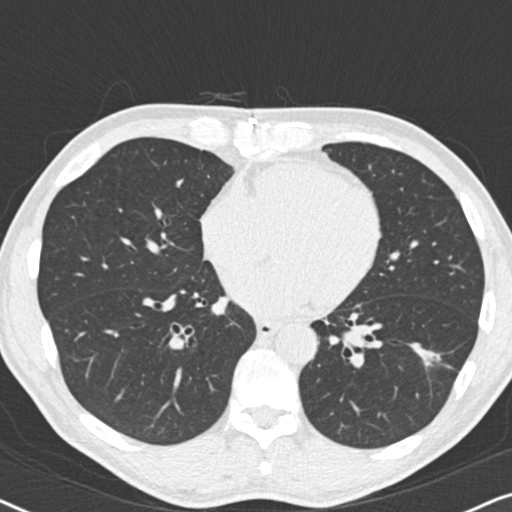
Axial slice from a low-dose chest CT screening exam; second screening round (one year after baseline); lung window (W 1500 / L -600 HU); 2 mm slice thickness; standard (soft-tissue) reconstruction kernel (B30f); 120 kVp; 512 × 512 image matrix. Male, age 59 years at enrolment. Current smoker at enrolment.
Expert reader's lesion annotation, bounding box [x1, y1, x2, y2] px = [410, 334, 466, 384]. The screening reader recorded 2 non-calcified nodules or masses ≥4 mm on this exam; which of them this box marks is not recorded. Official screen result: positive, other.